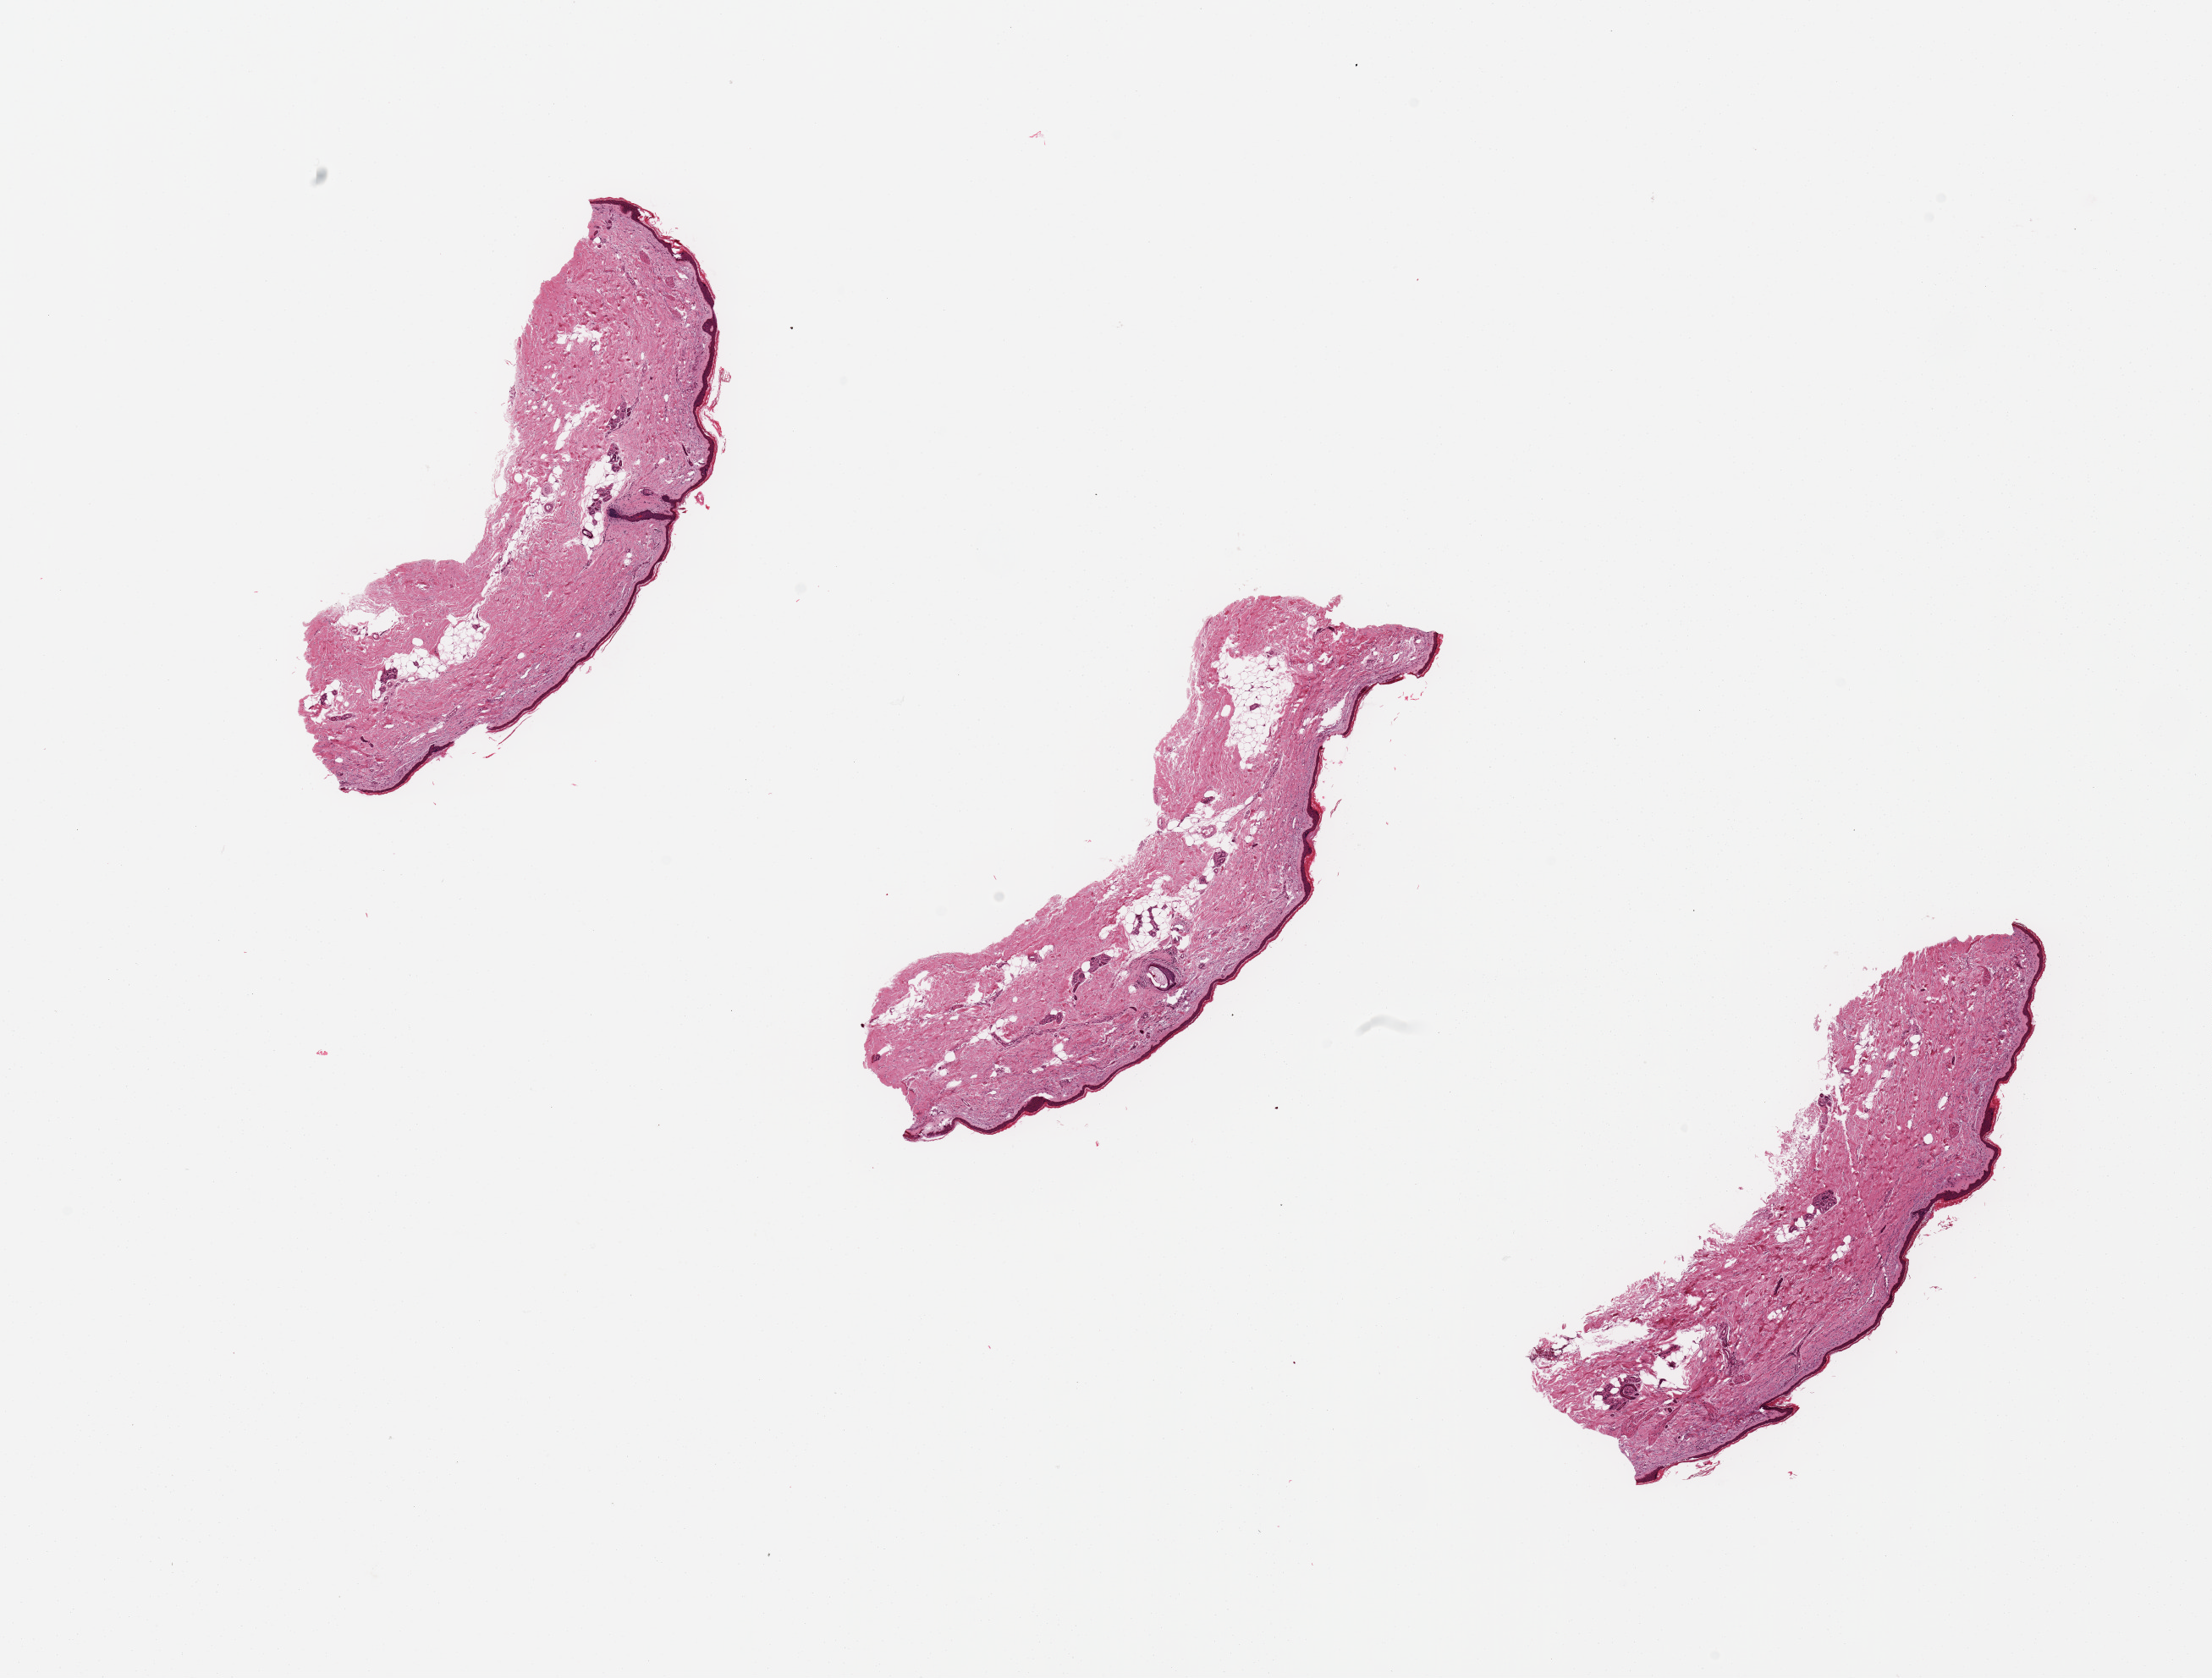
H&E whole-slide image, a low-resolution overview of the entire scanned area, about 20.7 x 15.7 mm (slide scanned at 20x). PAXgene-fixed, paraffin-embedded tissue. Target tissue: skin of lower leg. Tissue donor sample. Donor sex: female.
Review note (as recorded): 3 pieces. Epidermis is 1.5-2.5% of total specimen thickness (~1.5mm).